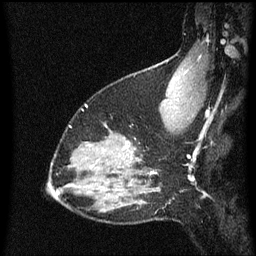
Breast MRI (dynamic contrast-enhanced), one sagittal slice; slice 47 of 60 in the series (ordered by position); dynamic contrast-enhanced series, image 2 of 3 at this slice position (ordered by acquisition); 1.5 T; TE 4.2 ms, TR 8.4 ms; 2 mm slice thickness; 256 × 256 image matrix, field of view 200 × 200 mm. Female patient, age 38 years. From the clinical record (not read from this slice): setting: breast cancer imaged before/during neoadjuvant chemotherapy; receptor status: HR-positive, HER2-negative.
Annotated regions visible in this slice (semi-automatically segmented with operator editing):
- analysis volume of interest (the breast-tissue region the enhancement analysis was run in; not a lesion): box from (x=122, y=126) to (x=144, y=163) px
- tumour enhancement mask (voxels above the 70 % enhancement threshold inside the analysis volume of interest): (x=124, y=146)–(x=136, y=153)